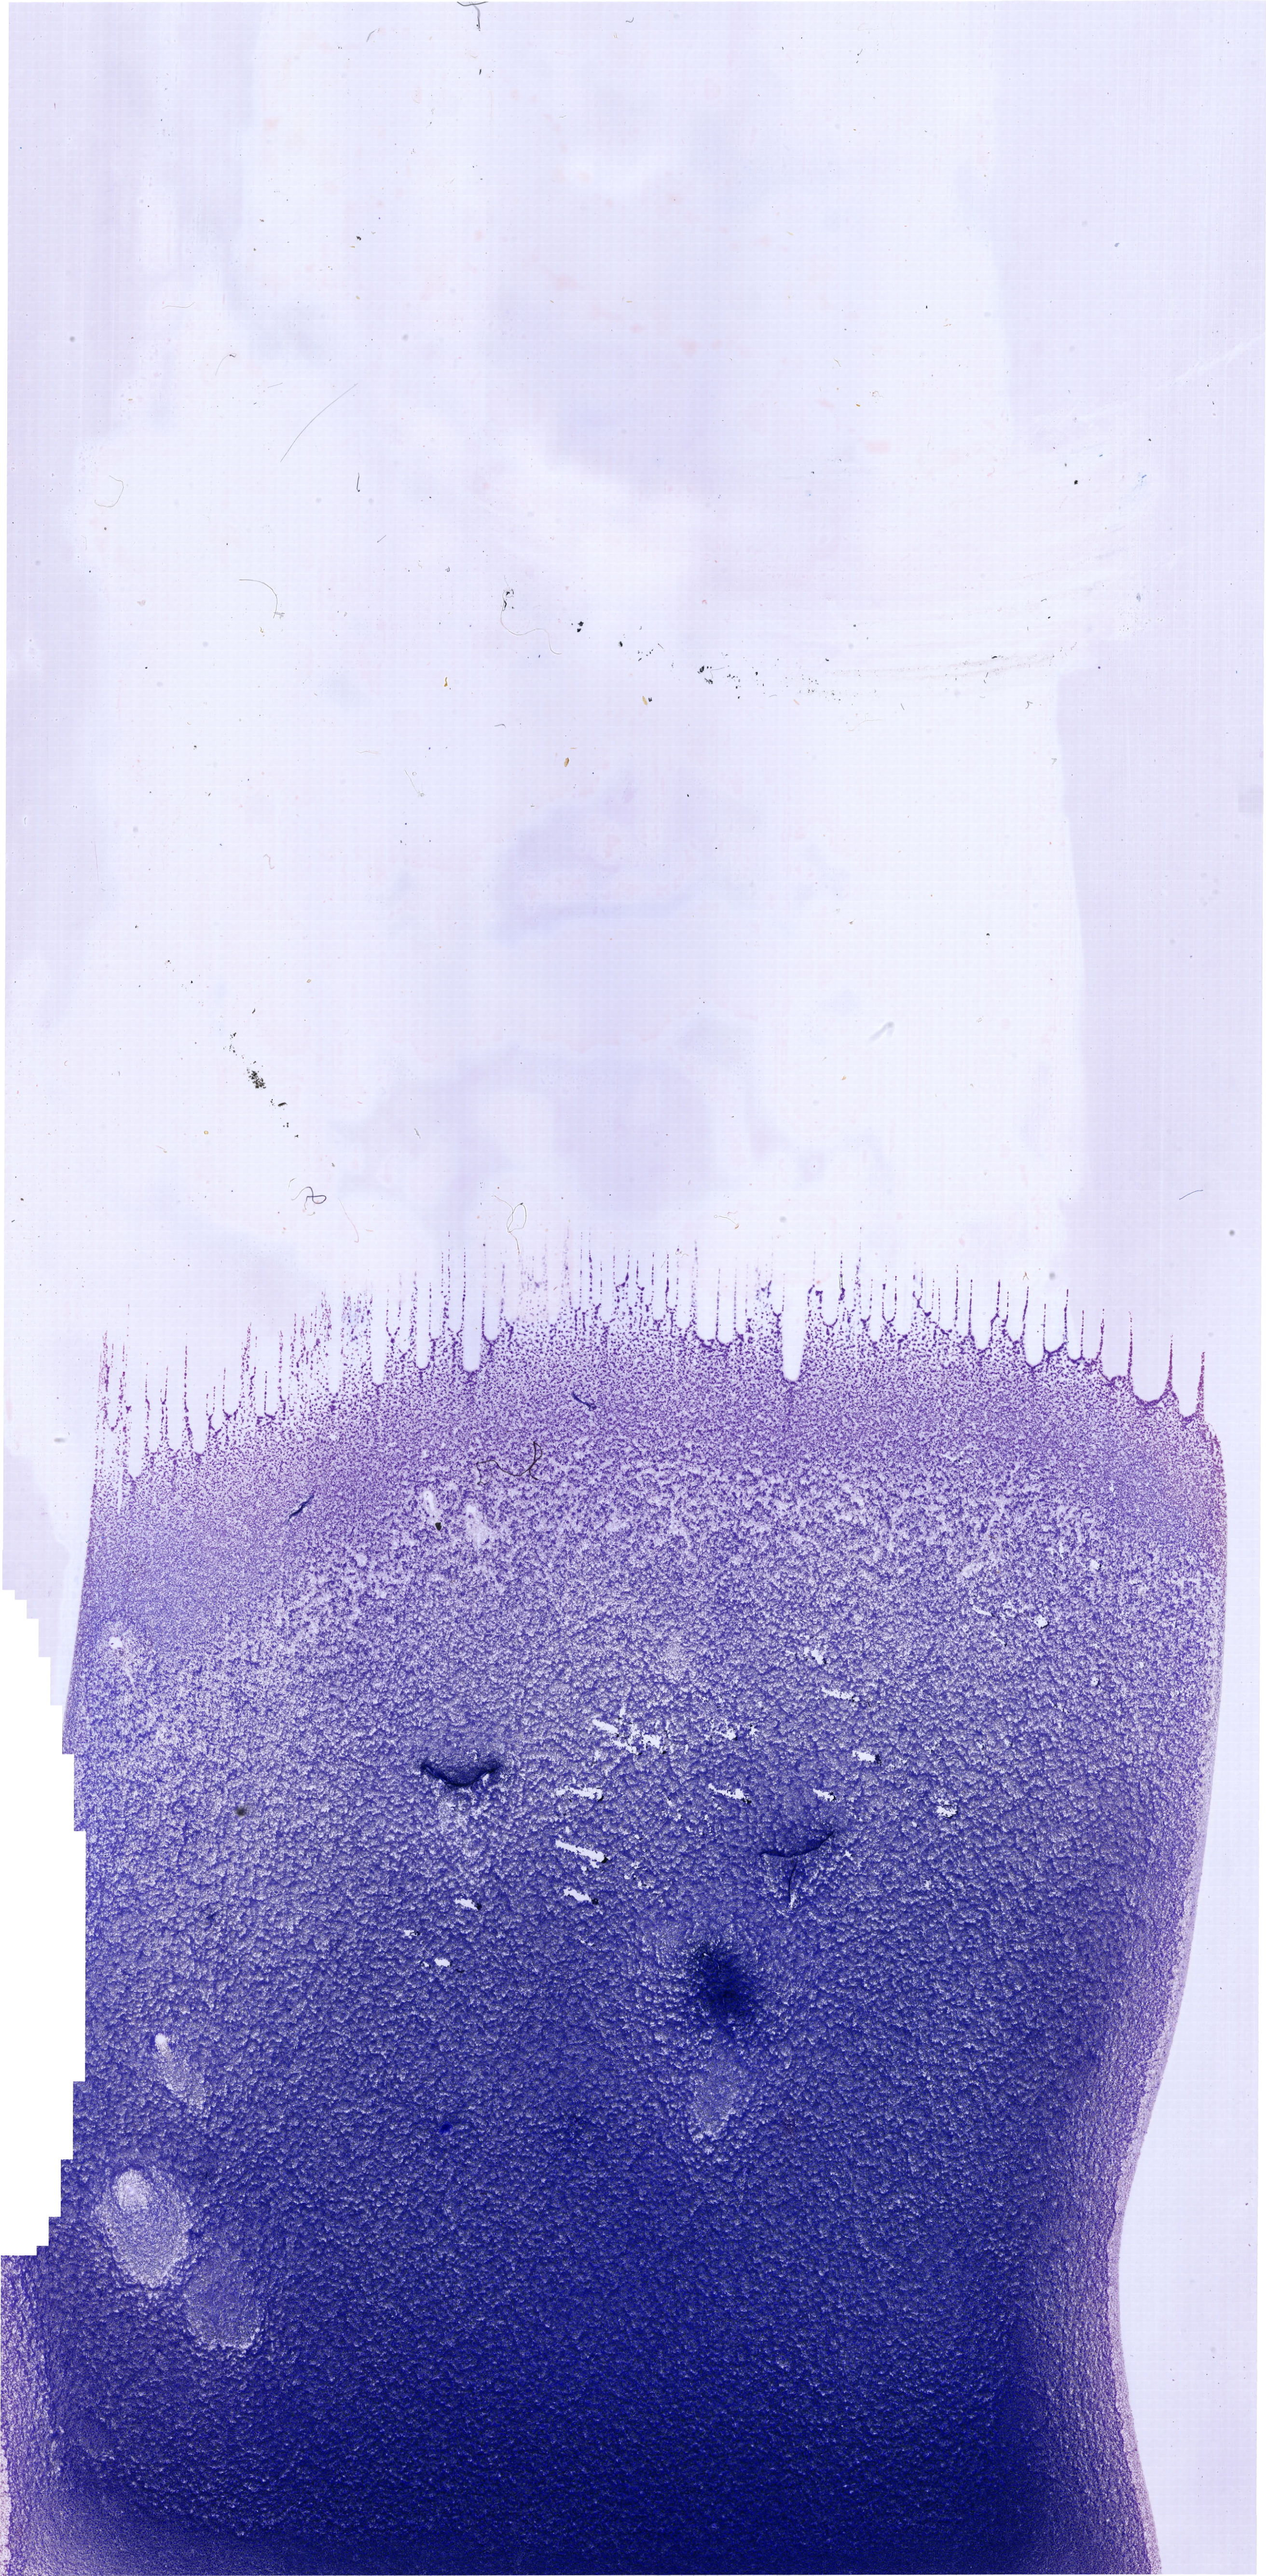
May-Grünwald-Giemsa (MGG)-stained marrow aspirate smear (whole slide), whole scanned area (about 20.5 x 41.7 mm) shown as a low-resolution overview. Male patient.
Diagnosis: T Acute Lymphoblastic Leukemia.